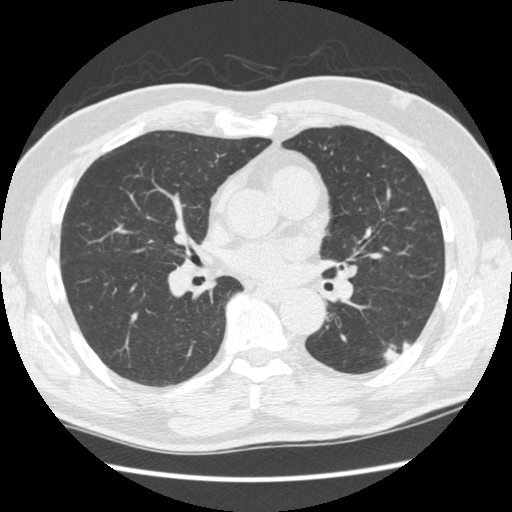
Chest CT (low-dose screening protocol), one axial image; baseline screening round; lung window (W 1500 / L -600 HU); standard (soft-tissue) reconstruction kernel (STANDARD); slice 126 of 267 in the series; 512 × 512 image matrix, field of view 360 × 360 mm. Male participant, aged 74 years at enrolment. Former smoker at enrolment.
- Lesion marked by an expert reader, bounding box [x1, y1, x2, y2] px = [374, 324, 416, 372].
- The screening reader recorded 3 non-calcified nodules or masses ≥4 mm on this exam (right upper lobe, right lower lobe, left upper lobe); which of them this box marks is not recorded.
- Official screen result: positive, change unspecified: nodule(s) >= 4 mm or enlarging nodule(s), mass(es), or other non-specific abnormalities suspicious for lung cancer.
- Participant outcome: lung cancer diagnosed 384 days after this screen — squamous cell carcinoma, NOS, left lower lobe, well differentiated (G1), stage IA (AJCC 6th edition), 28 mm at pathology.